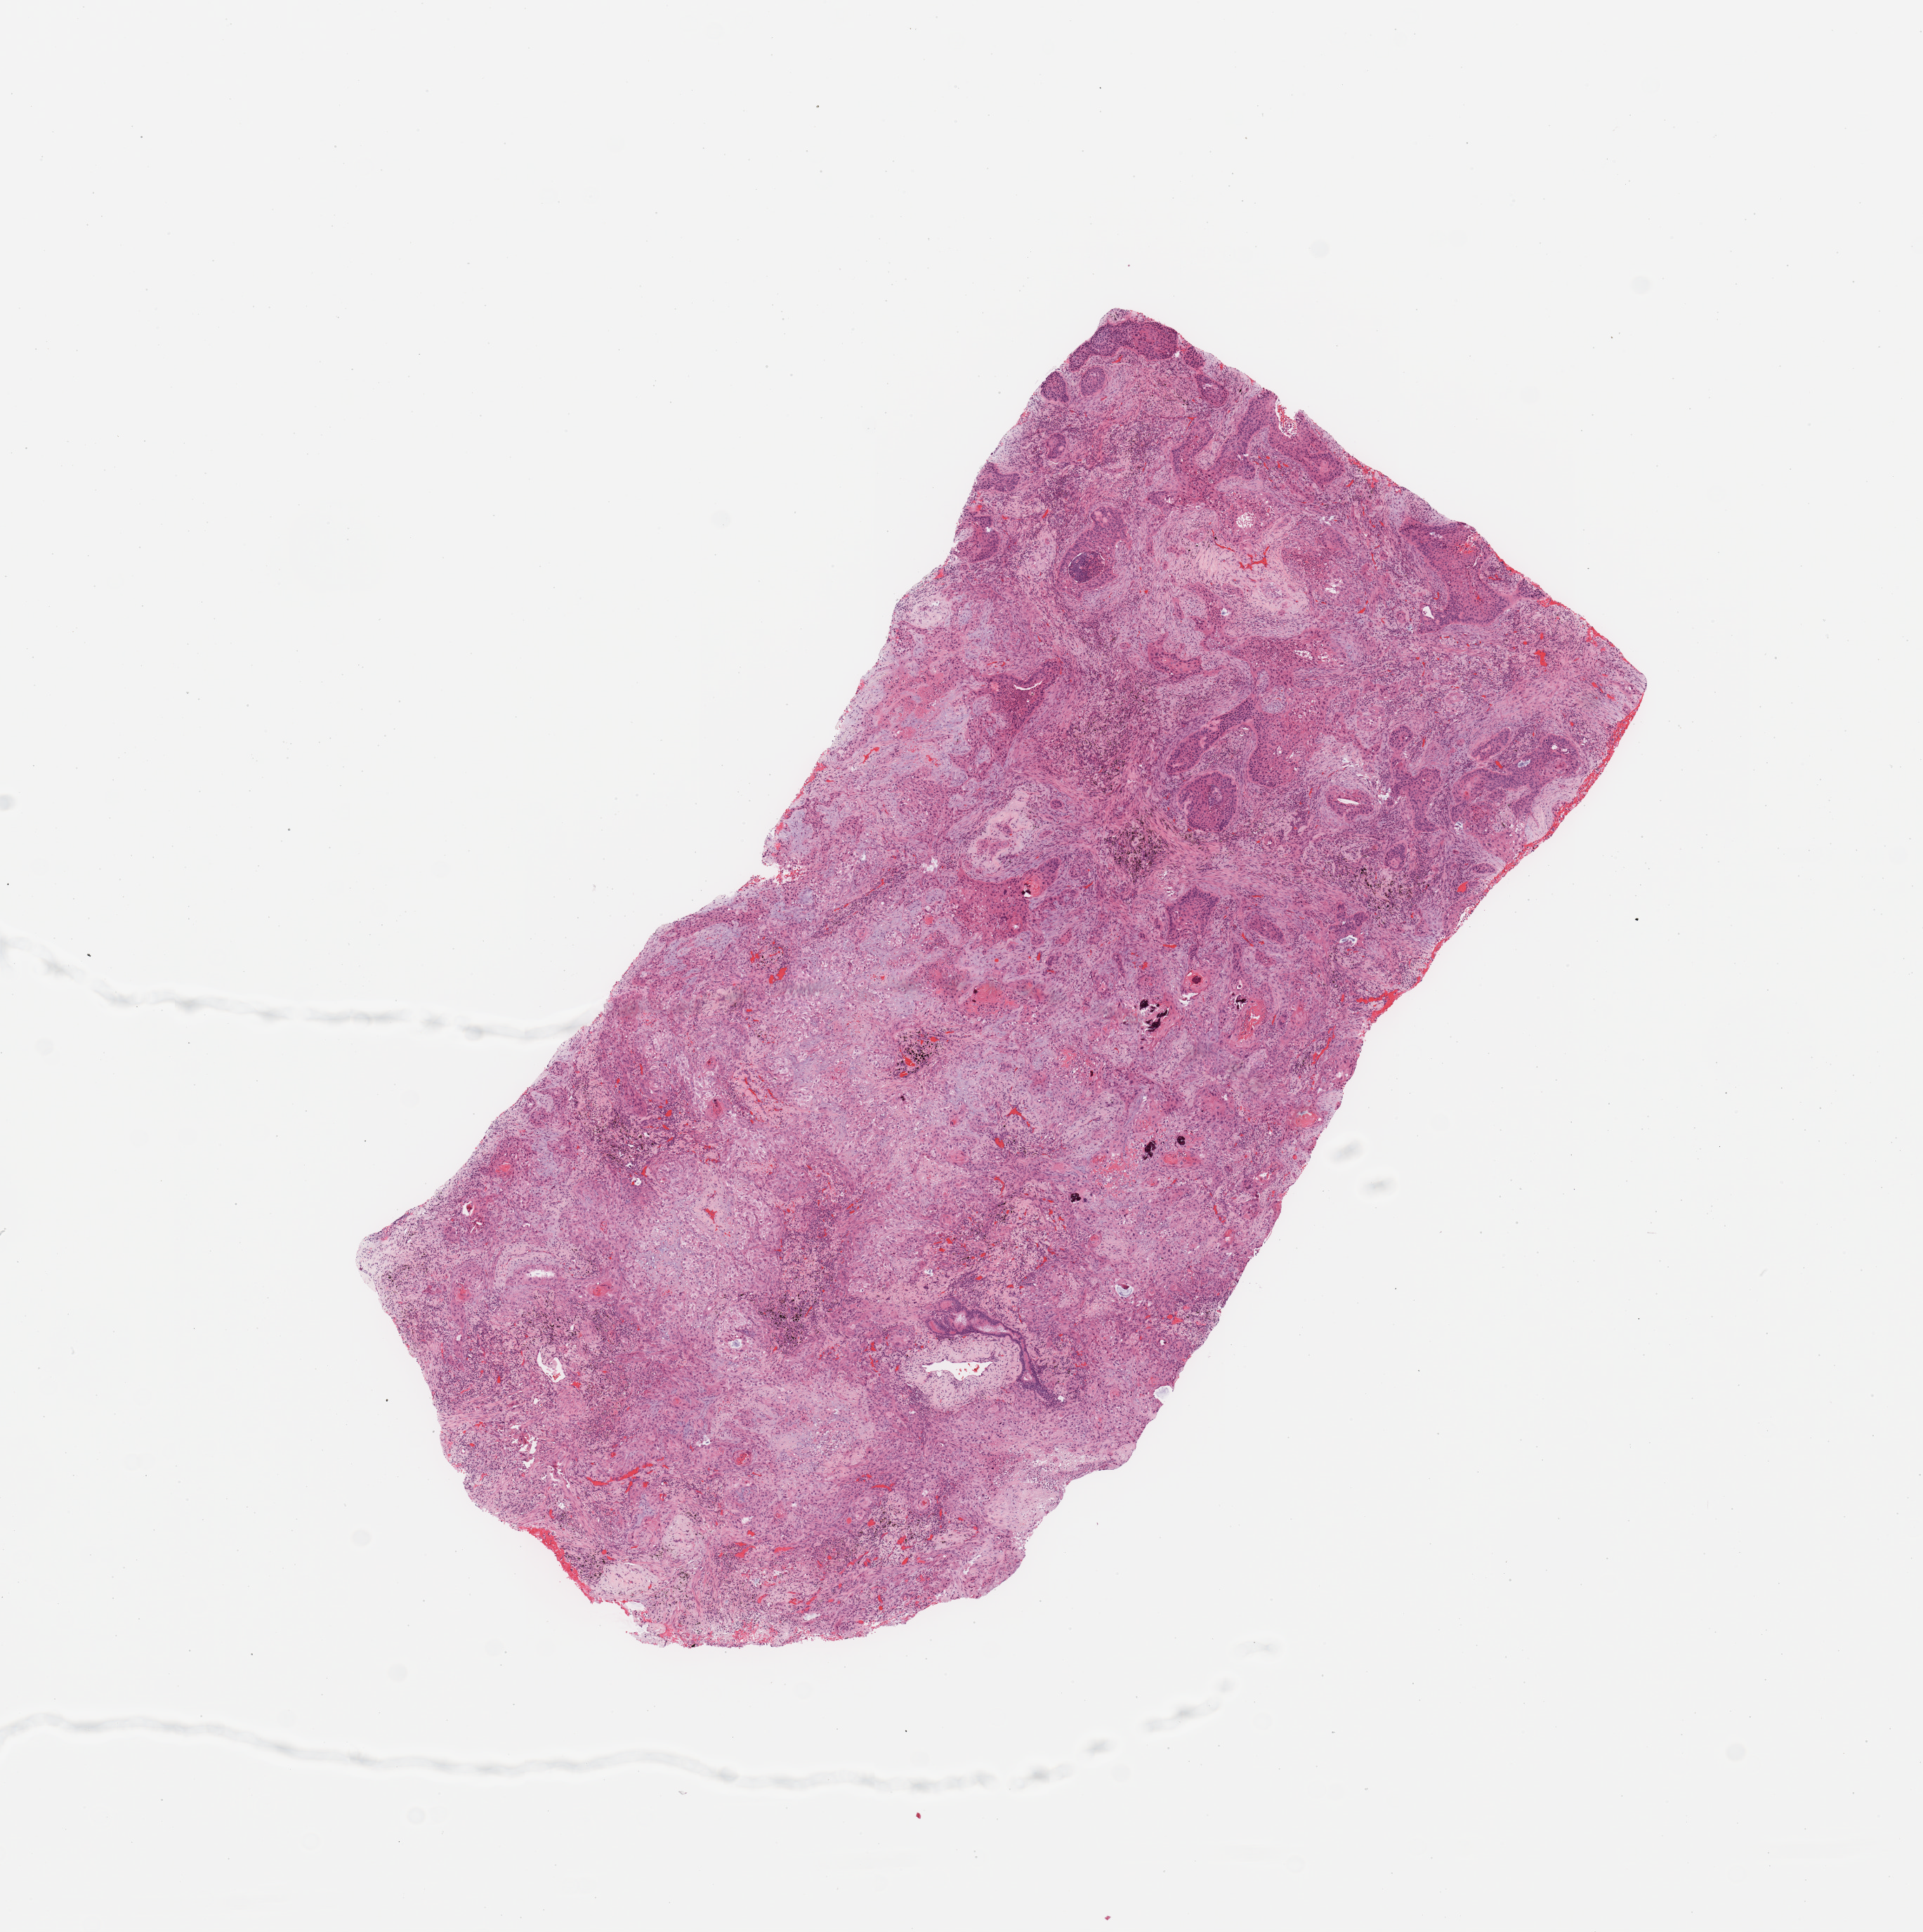
Whole-slide histology image, H&E, a low-resolution overview of the entire scanned area, about 10.8 x 10.9 mm (acquisition: 20x scan). Tumour tissue sample, sampled site: lung. Male, 70 y/o. Histologic grade: G2 (moderately differentiated). Composition of this section per pathologist review: tumour nuclei 60%, necrosis 15%.
AJCC pathologic stage: IB. Diagnosis: Squamous cell carcinoma, NOS.